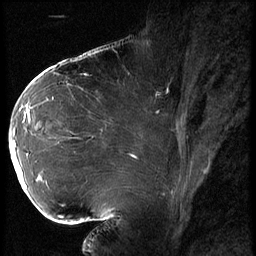
Breast MRI (dynamic contrast-enhanced), one sagittal slice. Position 37 of 62 along the scan axis. 3 images stored at this slice position (order not interpretable as contrast timing). 1.5 T. TE 4.2 ms, TR 9 ms. 2.5 mm slice thickness. 256 × 256 image matrix, field of view 180 × 180 mm. Female patient, age 43 years. Case-level facts recorded for this patient, not image findings: setting: breast cancer imaged before/during neoadjuvant chemotherapy; receptor status: HER2-positive.
Structures marked on this image (semi-automatically segmented with operator editing):
- analysis volume of interest (the breast-tissue region the enhancement analysis was run in; not a lesion): box from (x=10, y=90) to (x=82, y=203) px
- tumour enhancement mask (voxels above the 140 % enhancement threshold inside the analysis volume of interest): (x=11, y=103)–(x=41, y=189)